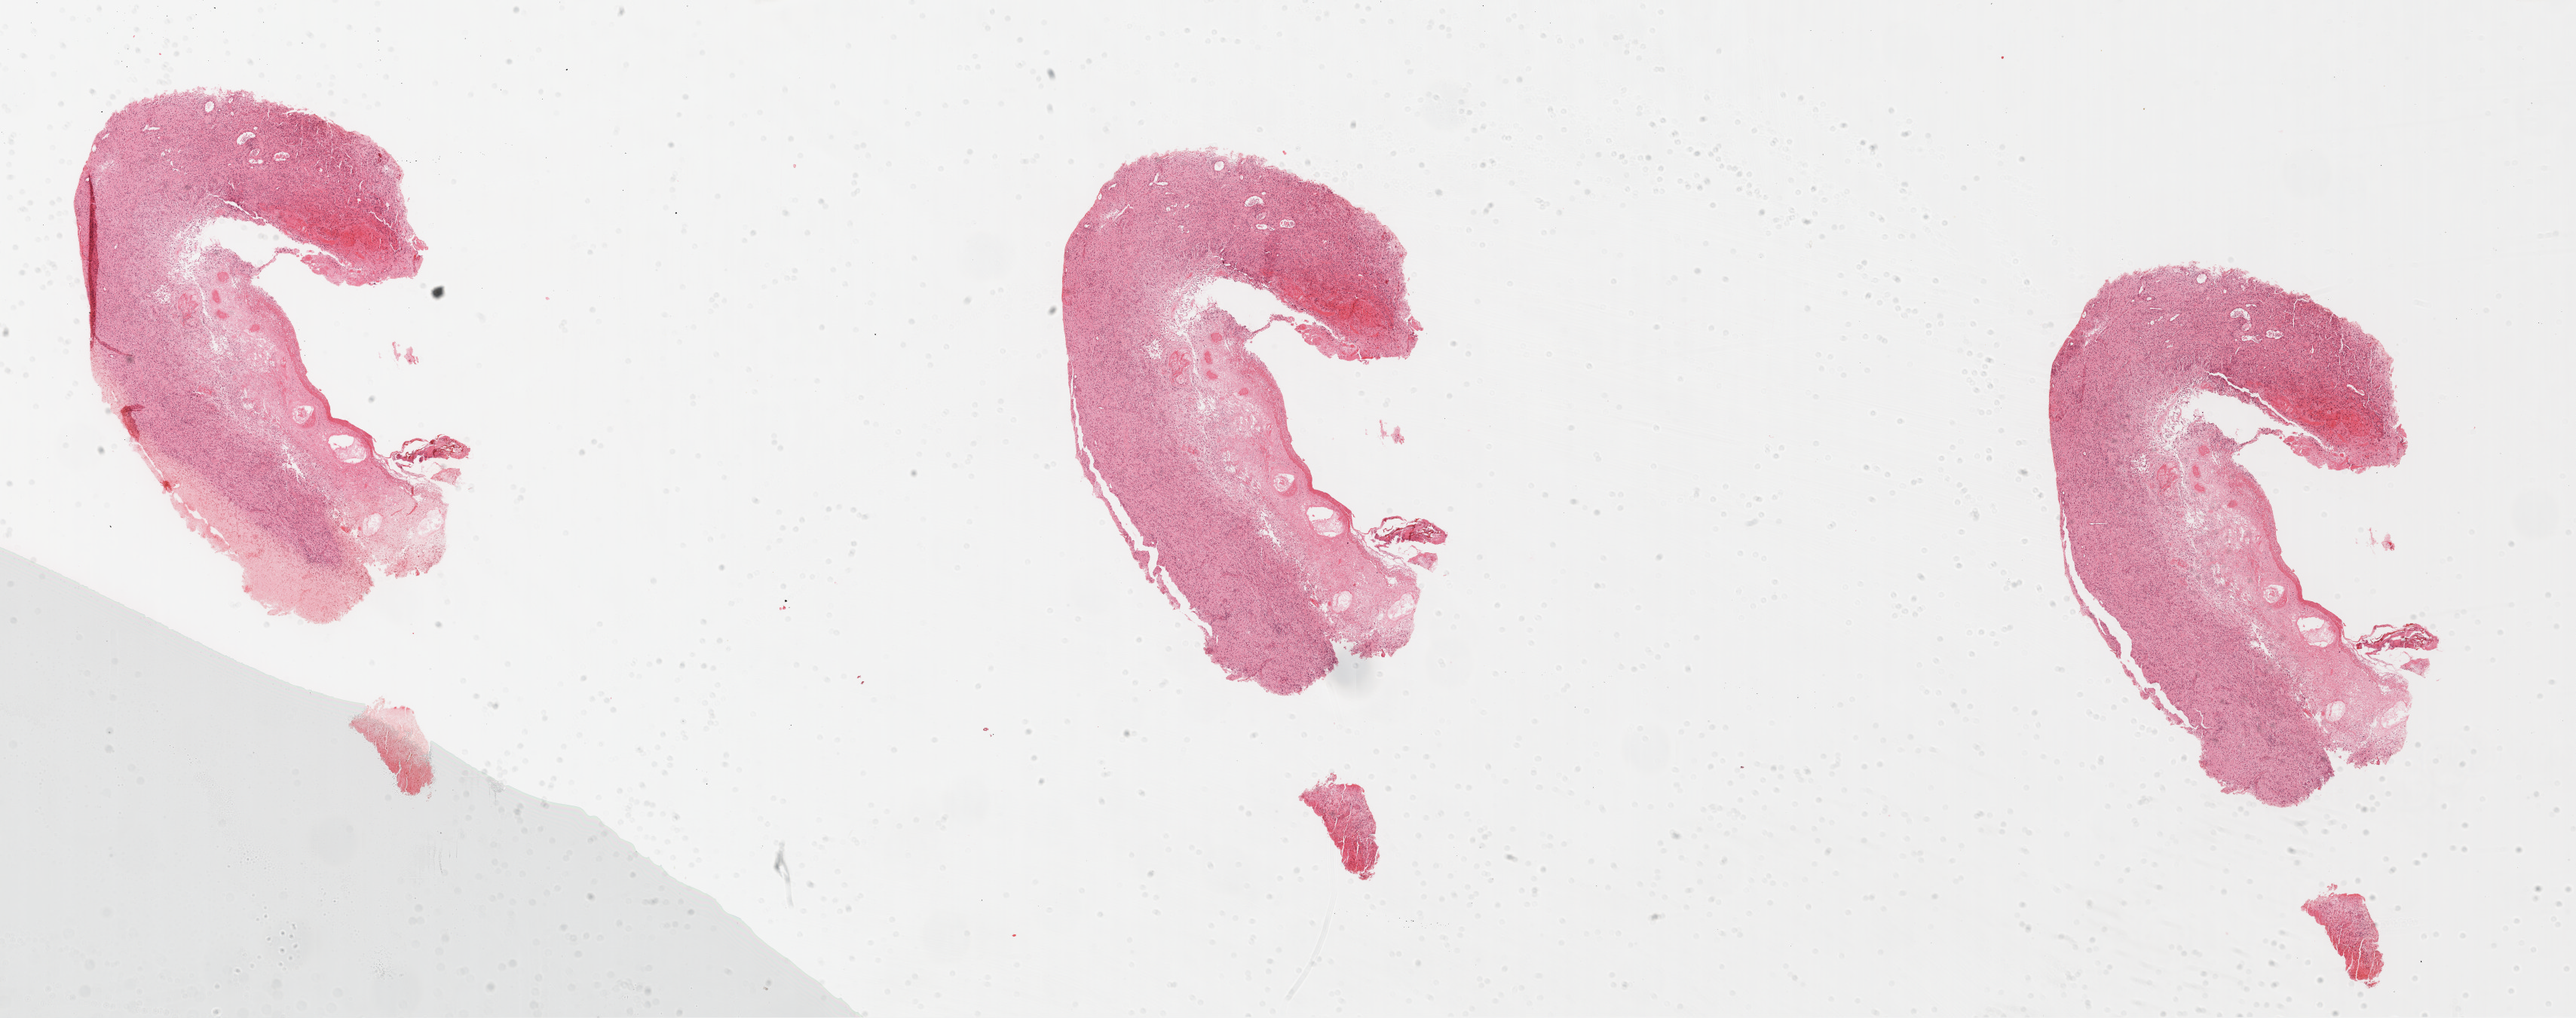
Whole-slide histology image, H&E — shown as a low-resolution overview of the whole scanned area (about 27.6 x 10.9 mm). Formalin-fixed paraffin-embedded (FFPE) diagnostic section. Brain, primary tumour sample. Patient: female, age at initial diagnosis 51 years.
• diagnosis: Glioblastoma